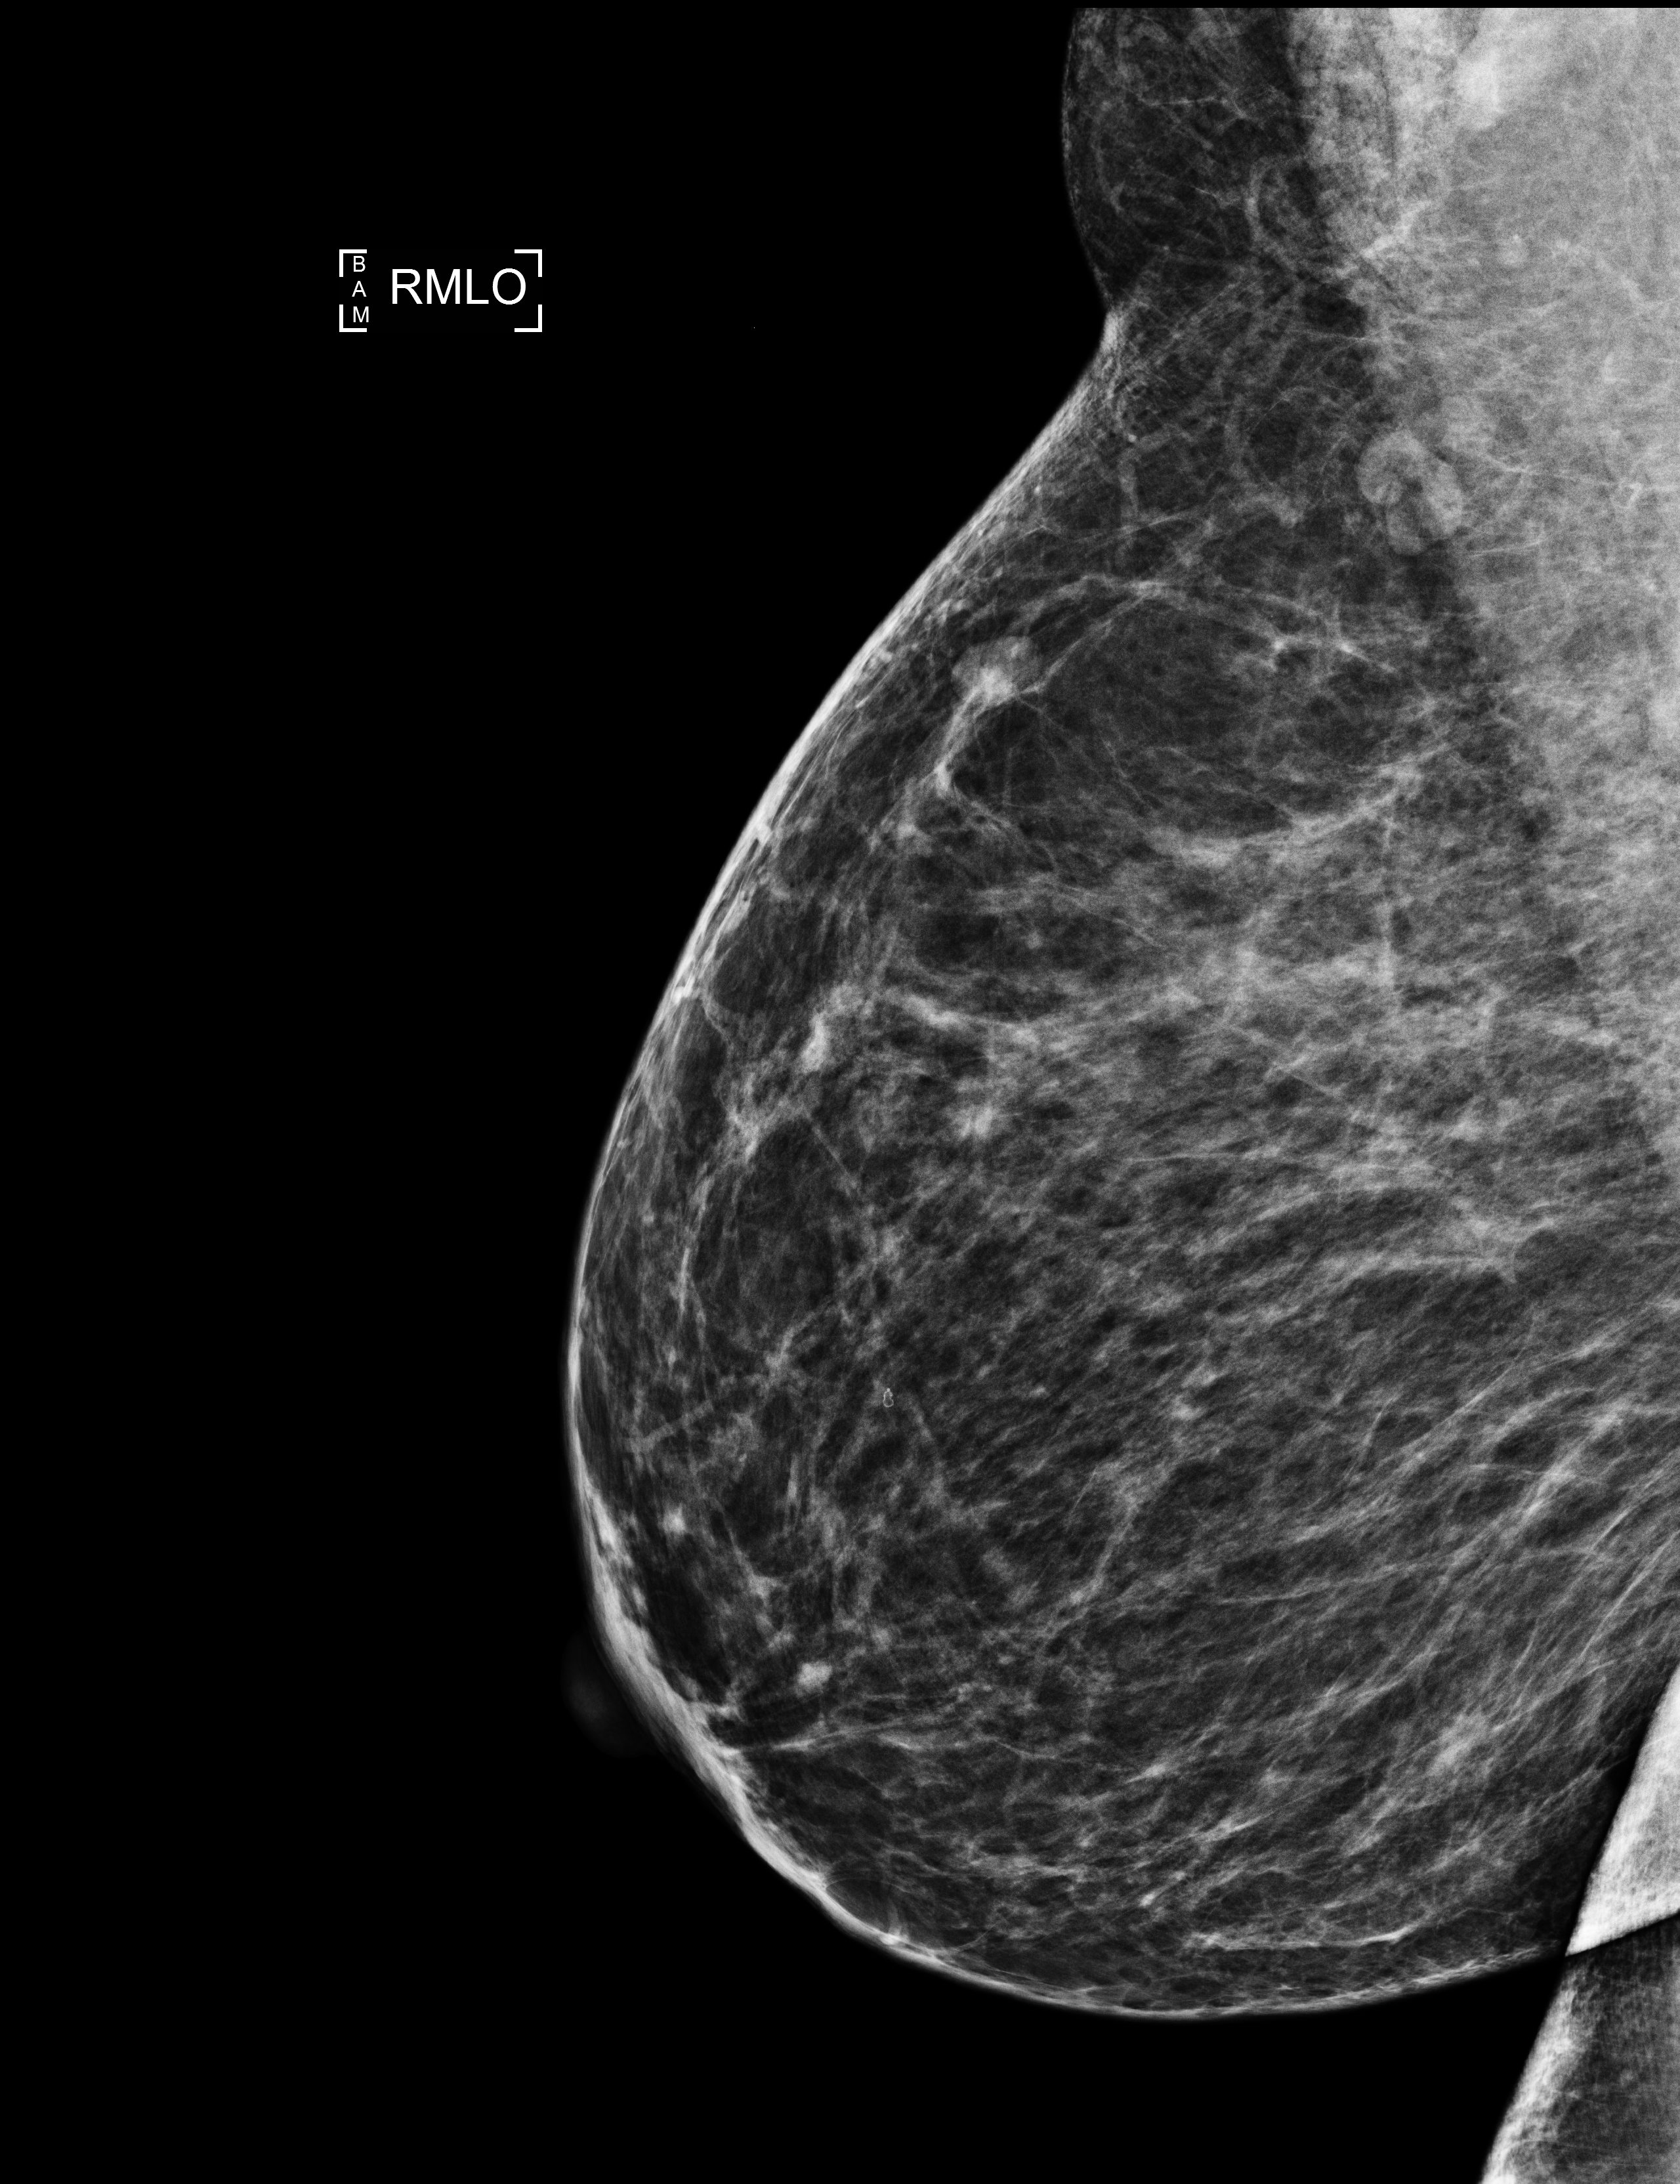
Annual screening mammography examination. Patient aged 45 years (female).
Image type: full-field digital mammogram. Breast: right. Projection: medio-lateral oblique projection.